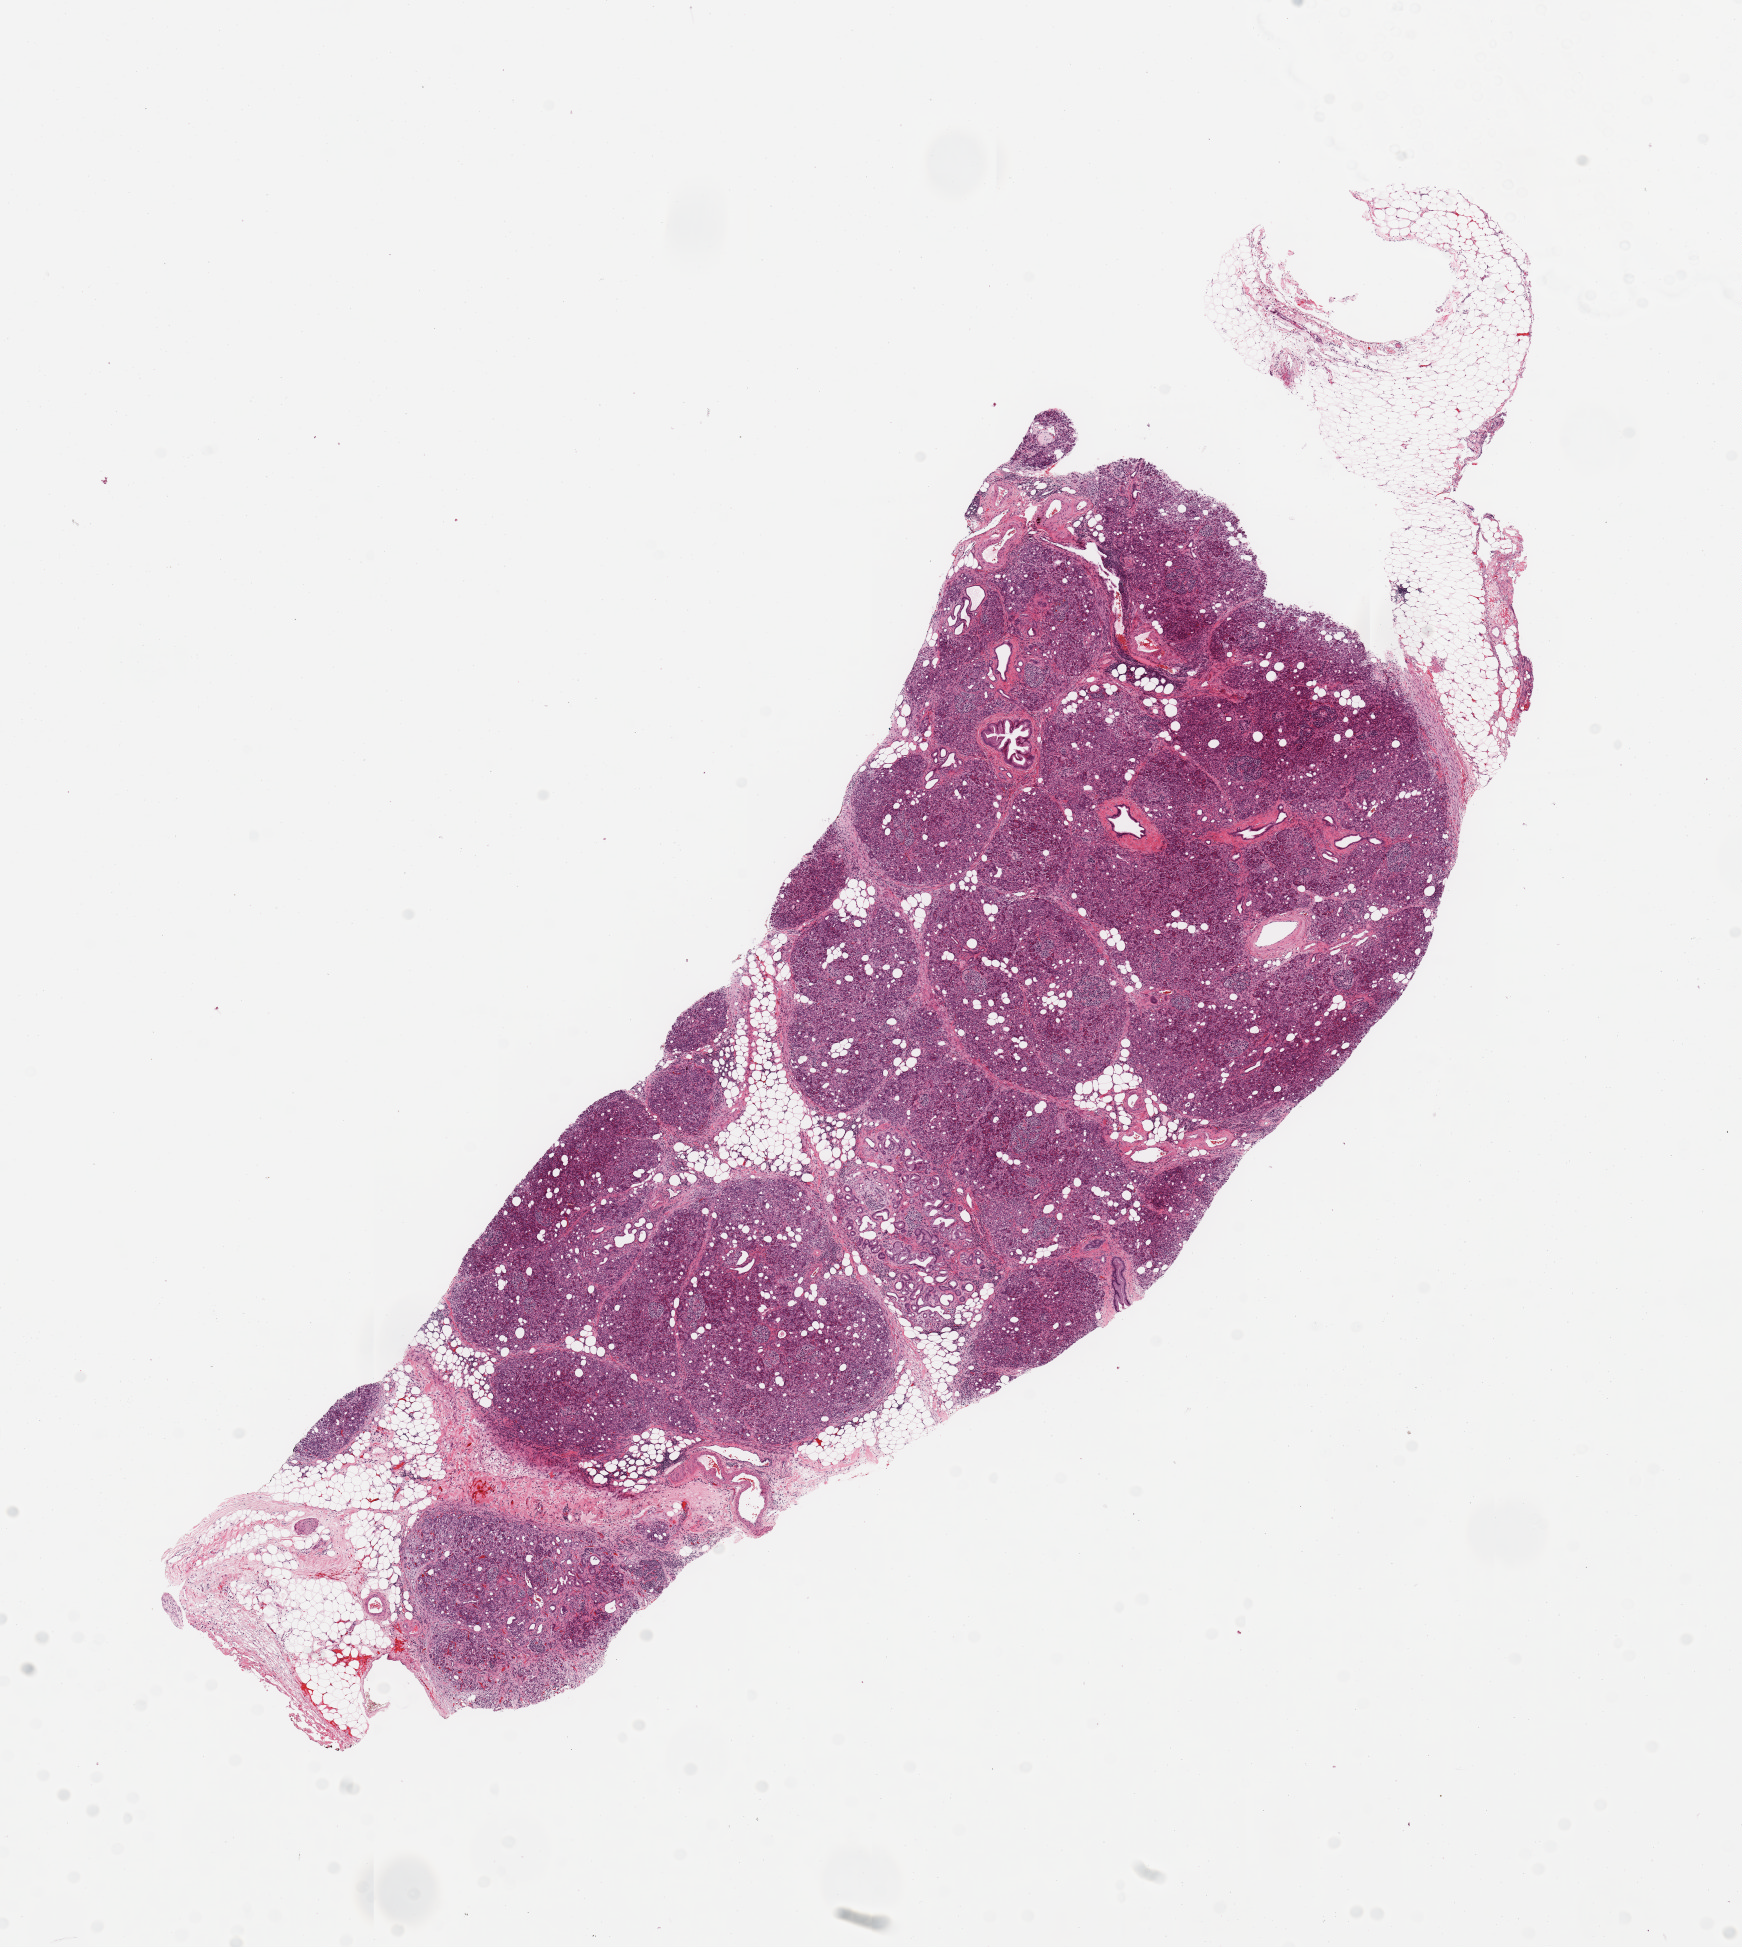
H&E whole-slide image, shown as a low-resolution overview of the whole scanned area (about 13.8 x 15.4 mm, from a 20x scan); normal (non-tumour) tissue sample, sampled site: pancreas. Male, 42 y/o.
• this section: normal (non-tumour) tissue from the same patient
• patient diagnosis: Infiltrating duct carcinoma, NOS